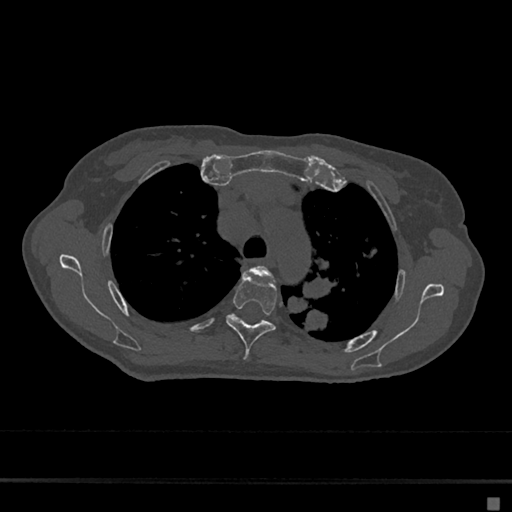
CT including the spine, one axial slice. Position 499 of 797 along the scan axis. Reconstruction kernel Br40s/3. 120 kVp. Bone window (W 1800 / L 400 HU). 512 × 512 image matrix. Female patient, age 68 years. Case-level facts recorded for this patient, not image findings: primary cancer: renal.
Annotated regions visible in this slice (semi-automatically segmented with operator editing):
- T3 vertebra: bounding box [x1, y1, x2, y2] px = [253, 266, 272, 278]
- T4 vertebra: [225, 274, 277, 361]
- T5 vertebra: [232, 316, 240, 321]